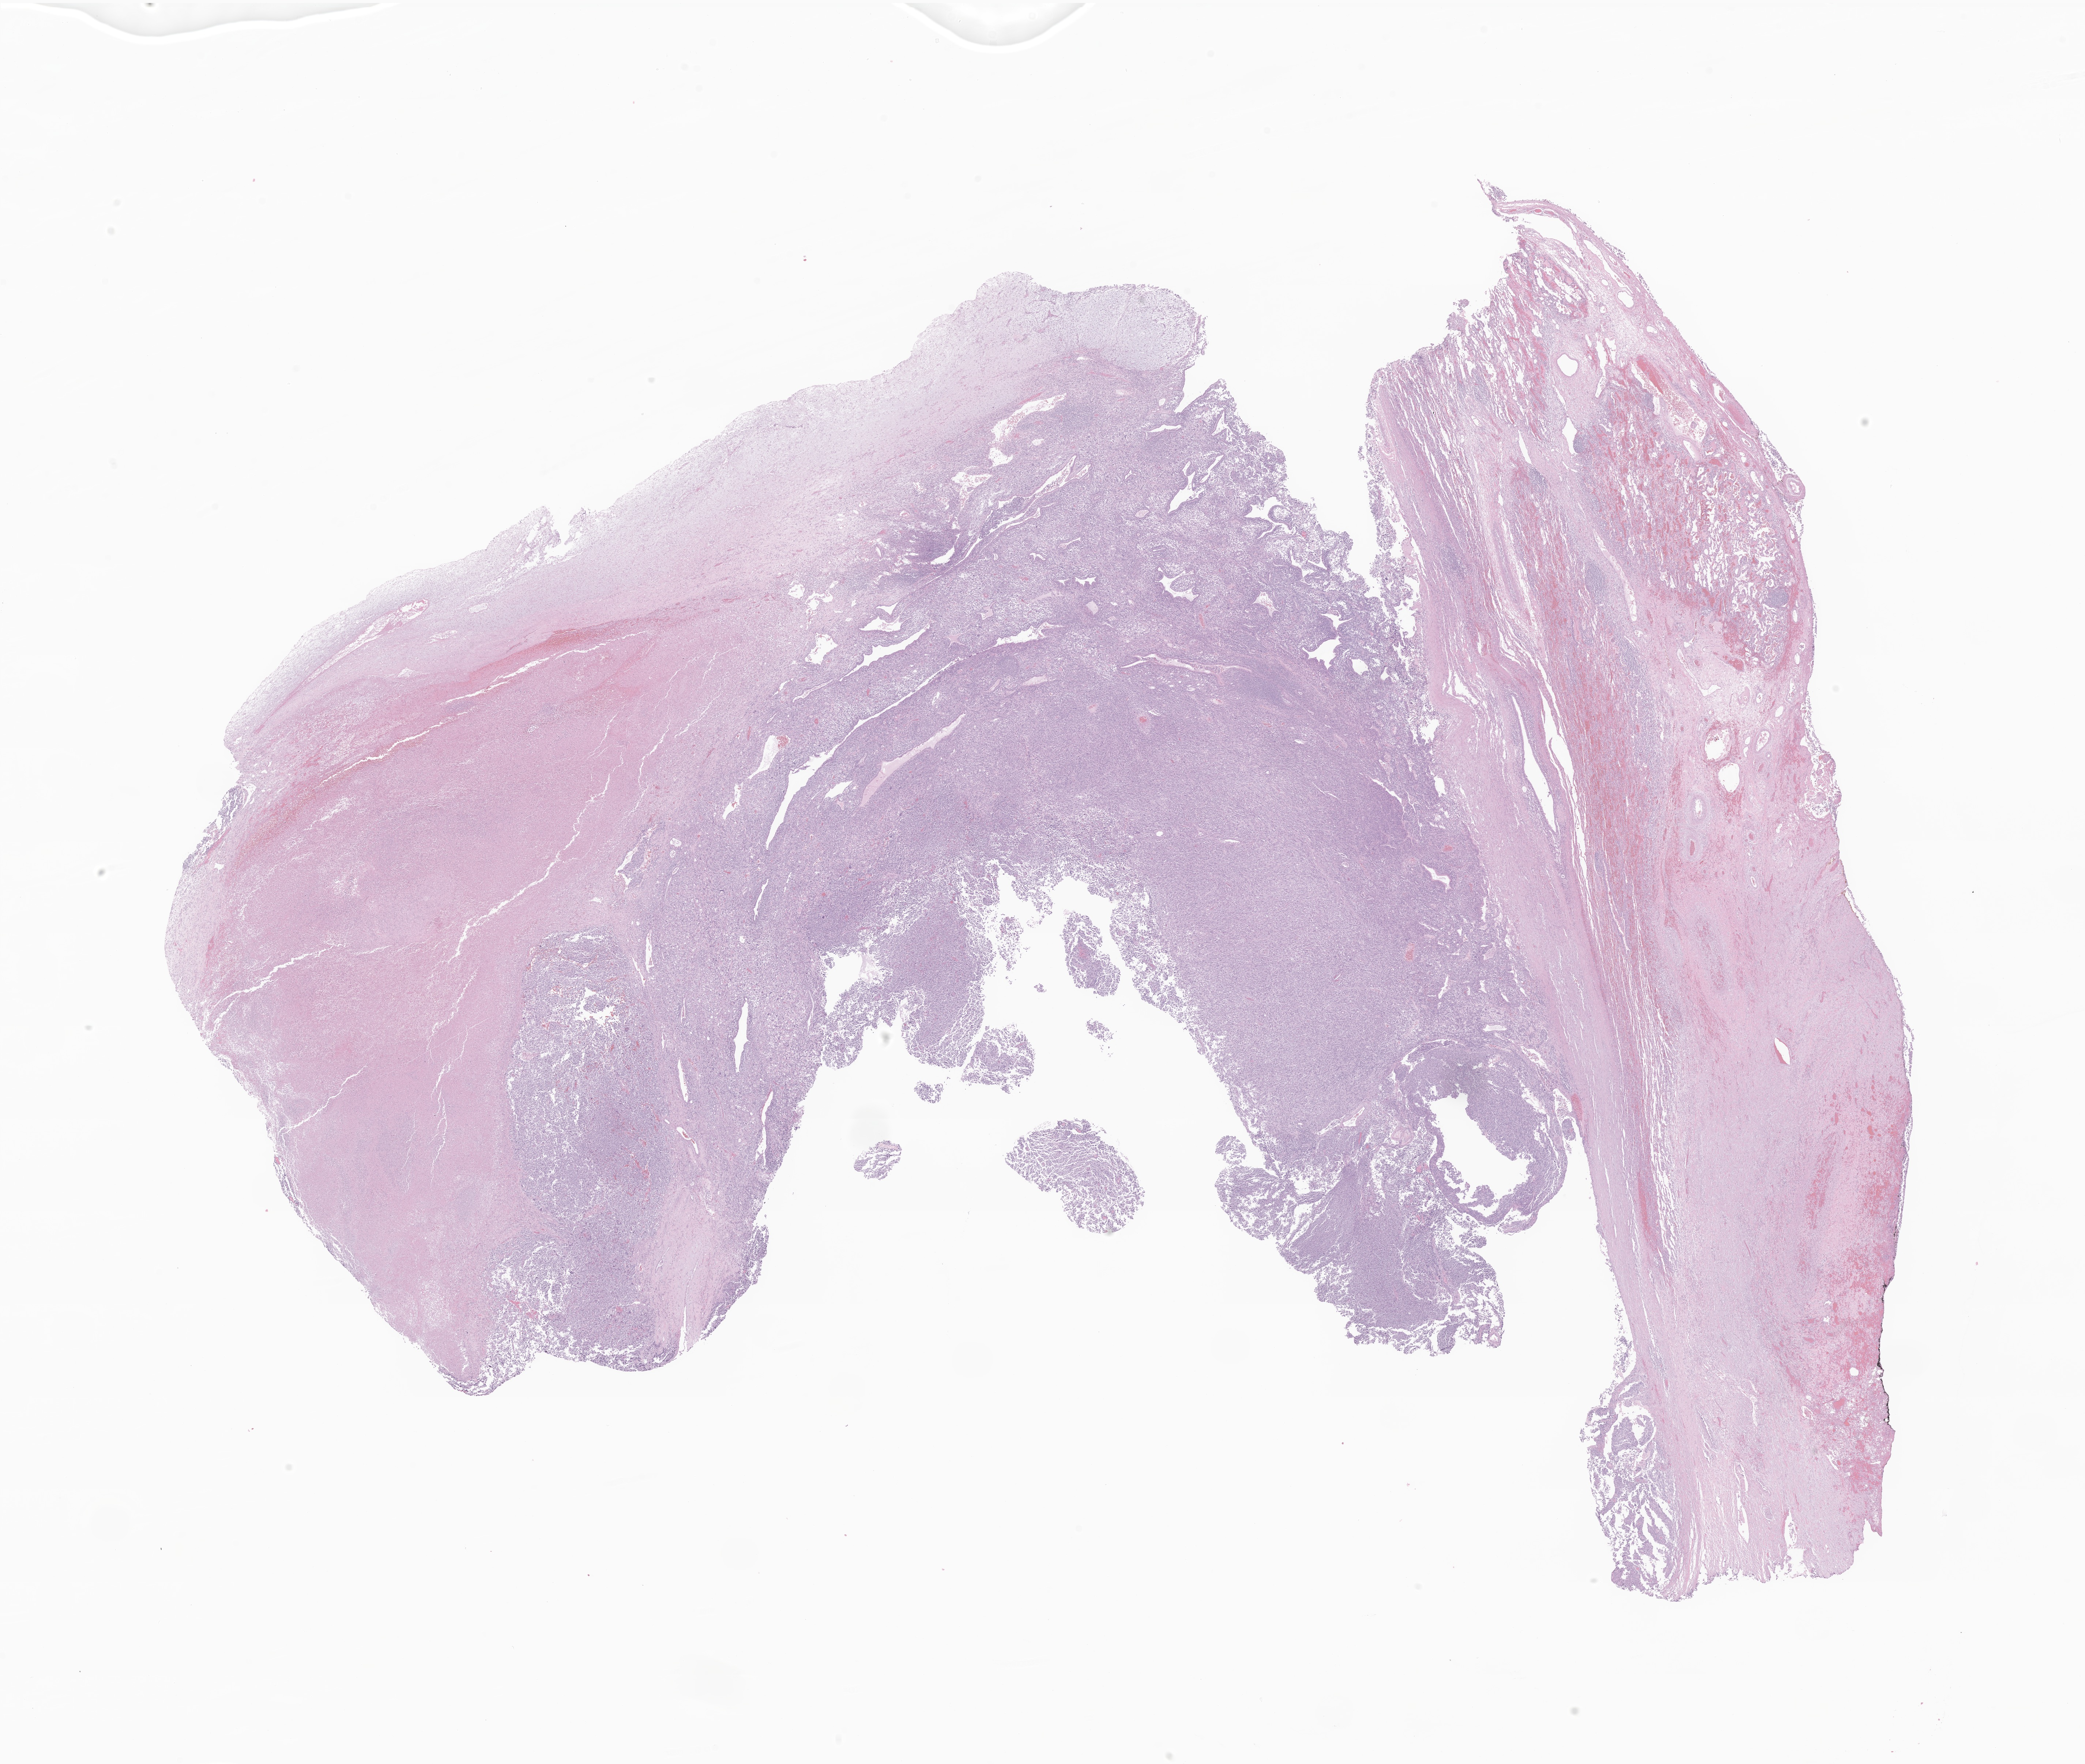
Whole-slide image, hematoxylin and eosin (H&E) stain of tumor tissue from the lung, a low-resolution overview of the entire scanned area, about 24.0 x 20.3 mm; formalin-fixed paraffin-embedded section. Patient female; age 731 days (about 2.0 years).
- recorded diagnosis: Pleuropulmonary blastoma